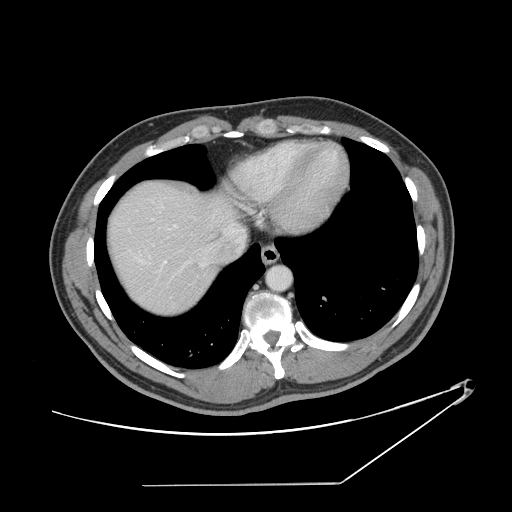
Contrast-enhanced abdominal CT, one axial slice; slice 130 of 152 in the series (ordered by position); 120 kVp; intravenous contrast given; soft-tissue window (W 400 / L 40 HU); 2.5 mm slice thickness; 512 × 512 image matrix, field of view 432 × 432 mm. Male patient, age 45 years. Case-level facts recorded for this patient, not image findings: diagnosis: colorectal cancer liver metastases, imaged before liver resection; multiple liver metastases: no; largest metastasis: 1 cm; disease in both lobes: no.
Structures marked on this image (manually delineated by an expert):
- hepatic veins: bounding box <128,205,243,267> (left, top, right, bottom; pixels)
- liver: <110,183,230,314>
- planned liver remnant (the part of the liver to remain after resection): <110,183,228,314>